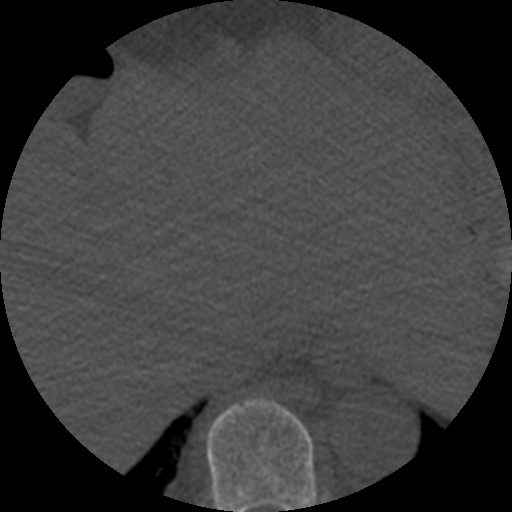
CT including the spine, one axial slice. Position 292 of 508 along the scan axis. Bone window (W 1800 / L 400 HU). 1.25 mm slice thickness. 512 × 512 image matrix, field of view 160 × 160 mm. Patient age 57 years. Case-level facts recorded for this patient, not image findings: primary cancer: prostate.
Outlined on this slice (semi-automatic segmentation, software-assisted and operator-edited):
- T9 vertebra: bounding box [x1, y1, x2, y2] px = [206, 397, 316, 512]